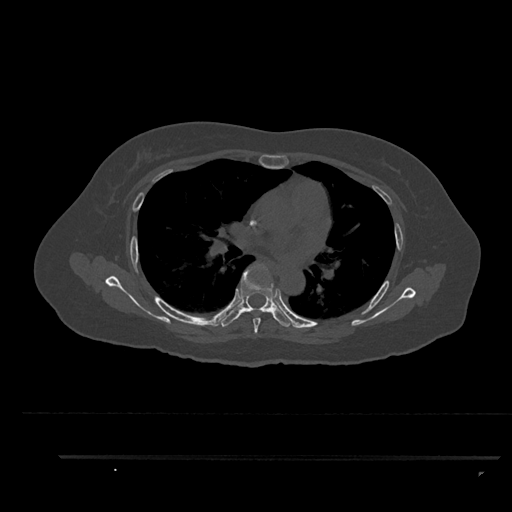
CT including the spine, one axial slice; position 575 of 797 along the scan axis; 120 kVp; bone window (W 1800 / L 400 HU); 0.5 mm slice thickness; 512 × 512 image matrix, field of view 408 × 408 mm. Female patient, age 44 years. From the clinical record (not read from this slice): primary cancer: renal; vertebrae with lytic lesions (as recorded): L1.
Structures marked on this image (semi-automatically segmented with operator editing):
- T5 vertebra: bounding box [x1, y1, x2, y2] px = [253, 268, 268, 333]
- T6 vertebra: [221, 264, 295, 328]